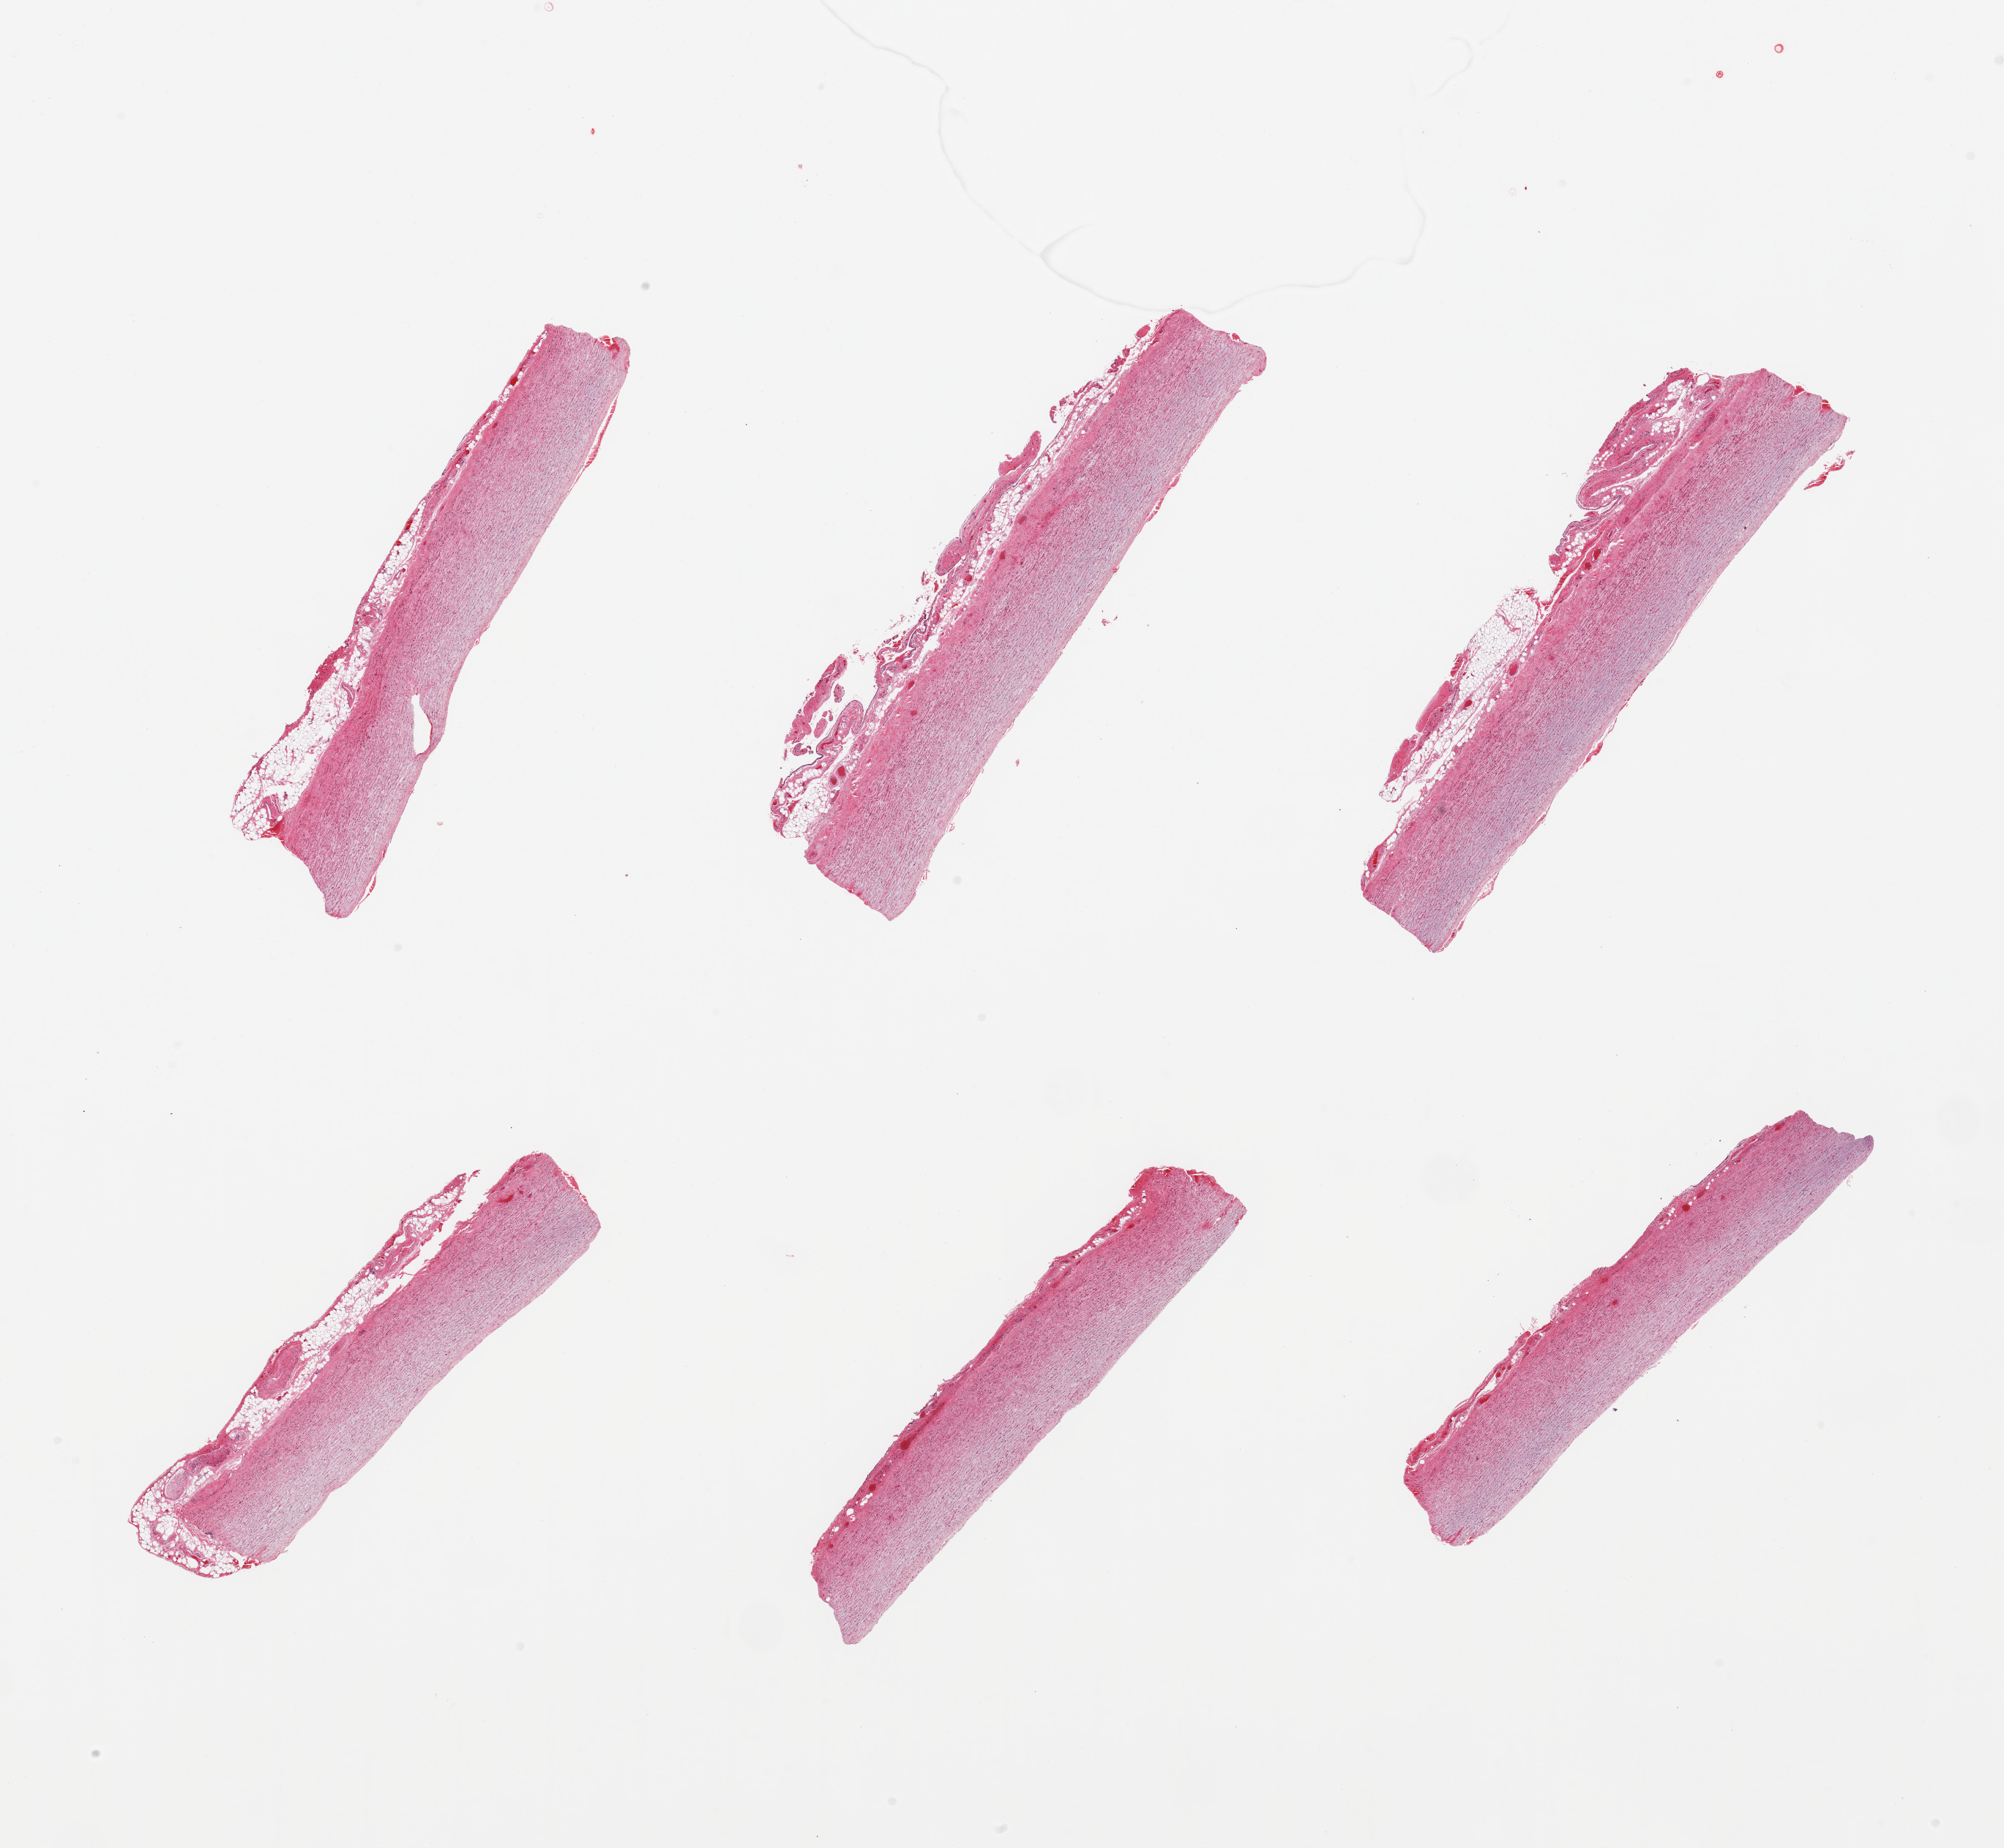
Haematoxylin and eosin whole-slide image, whole scanned area (about 21.7 x 20.0 mm, acquisition: 20x scan) shown as a low-resolution overview; PAXgene-fixed paraffin-embedded (PFPE) section; target tissue: aorta; donor tissue sample. Donor sex: female.
Pathologist's review note for this sample: 6 pieces; myxoid degeneration.